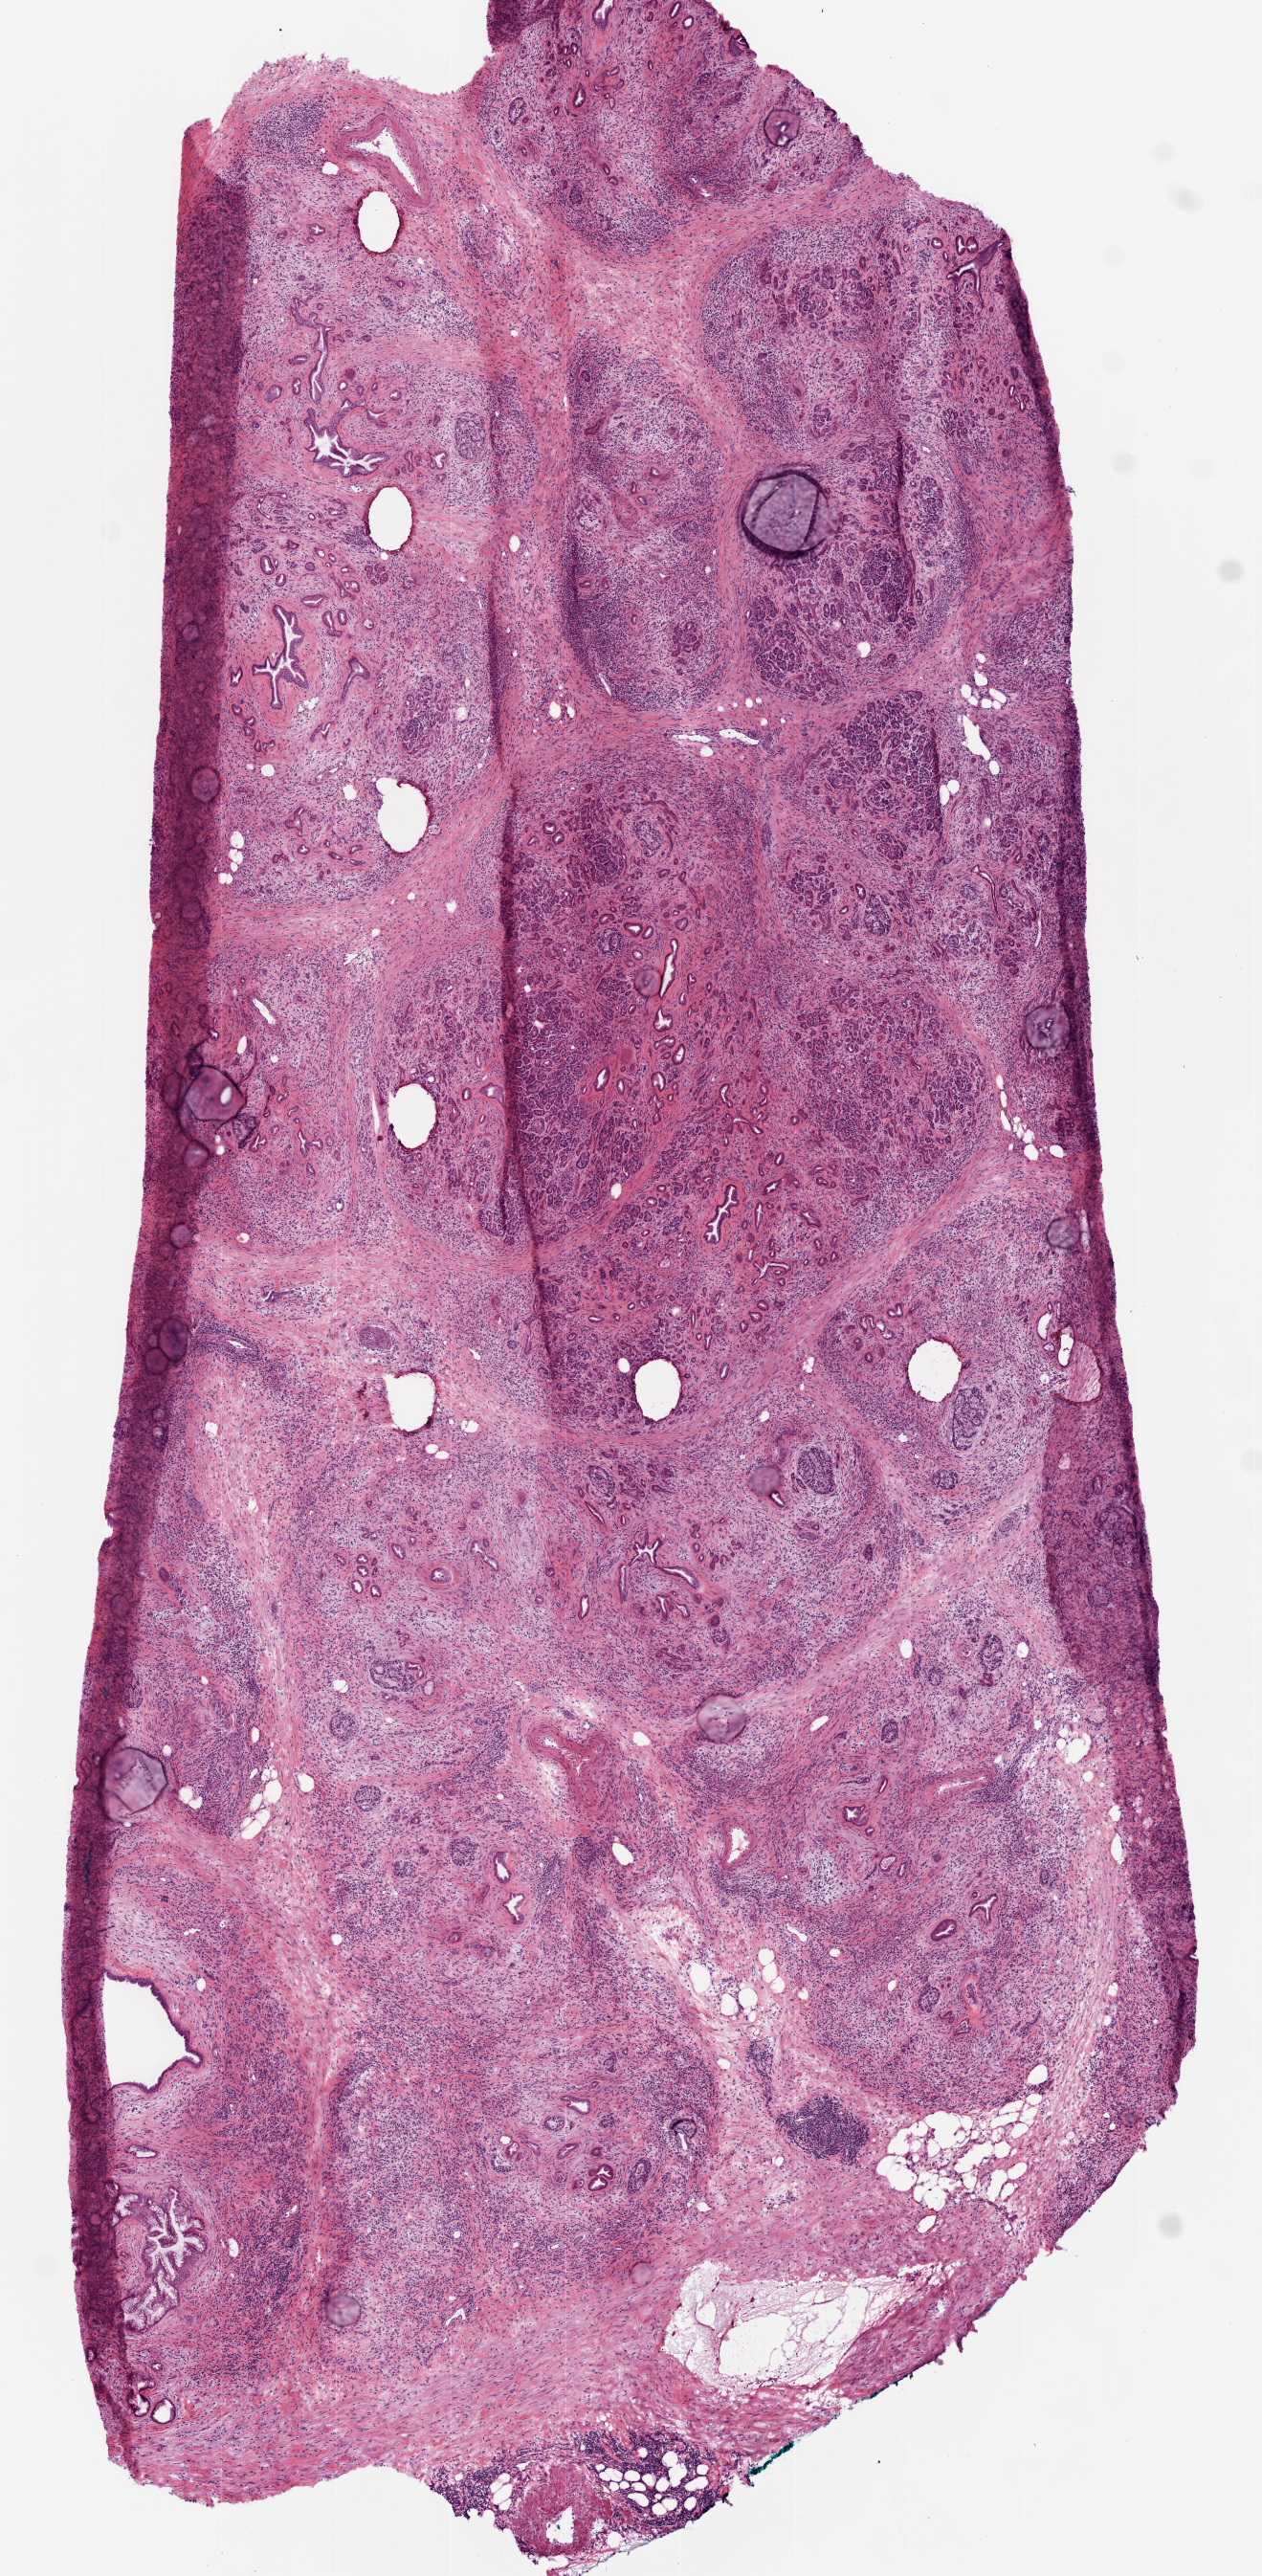
Hematoxylin and eosin (H&E) stained whole-slide image — whole scanned area (about 5.3 x 10.9 mm, from a 20x scan) shown as a low-resolution overview, frozen section, primary tumour sample from the pancreas. Male patient; age at initial diagnosis 54 years. Histologic grade: G3 (poorly differentiated). Composition of this section per pathologist review: tumour nuclei 5%, necrosis 0%.
AJCC pathologic stage: IIB (7th edition). Diagnosis: Adenocarcinoma, NOS.